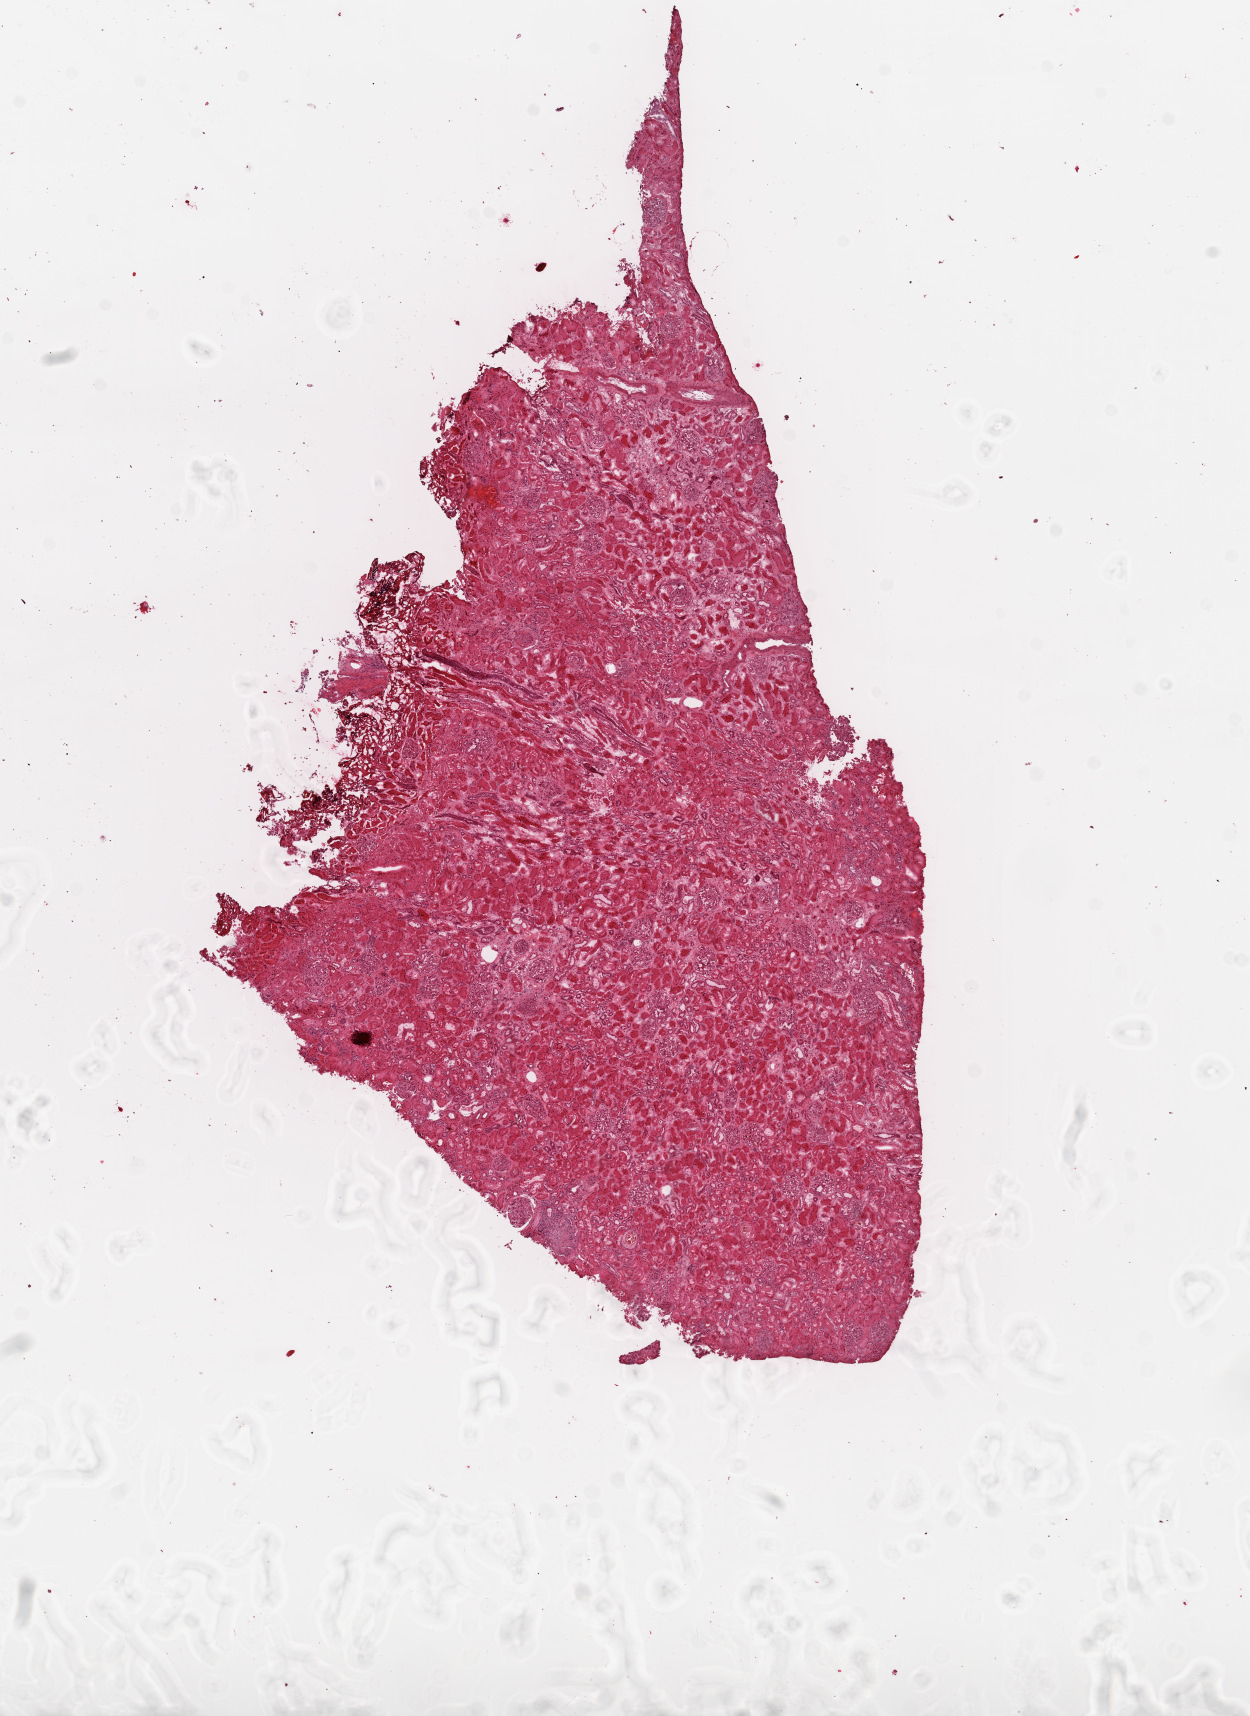
H&E whole-slide image, low-resolution overview of the scanned area, about 10.0 x 13.8 mm (from a 20x scan); frozen section; kidney, solid tissue normal (non-tumour tissue) sample. Patient: male, age at initial diagnosis 52 years.
• this section: solid tissue normal (non-tumour) sample from the same patient
• patient diagnosis: Clear cell adenocarcinoma, NOS